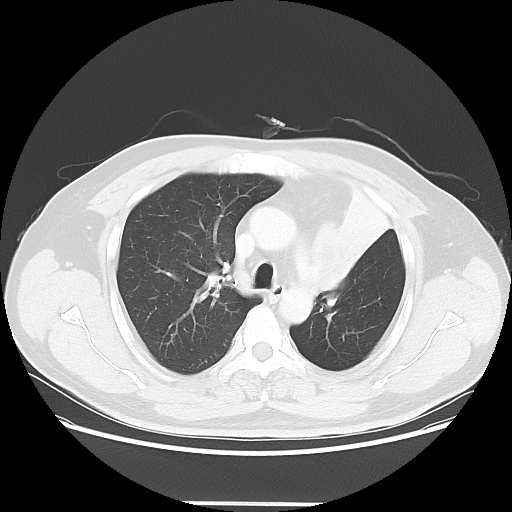
Chest CT, one axial slice. Slice 42 of 62 in the series (ordered by position). Reconstruction kernel LUNG. Lung window (W 1500 / L -600 HU). 5 mm slice thickness. 512 × 512 image matrix, field of view 403 × 403 mm. Male patient, age 49 years. Case-level facts recorded for this patient, not image findings: clinical TNM (as recorded): T3 N3 M1c.
Outlined on this slice (bounding box drawn by a radiologist):
- lung tumour (recorded histology: squamous cell carcinoma): bounding box <306,223,354,296> (left, top, right, bottom; pixels)